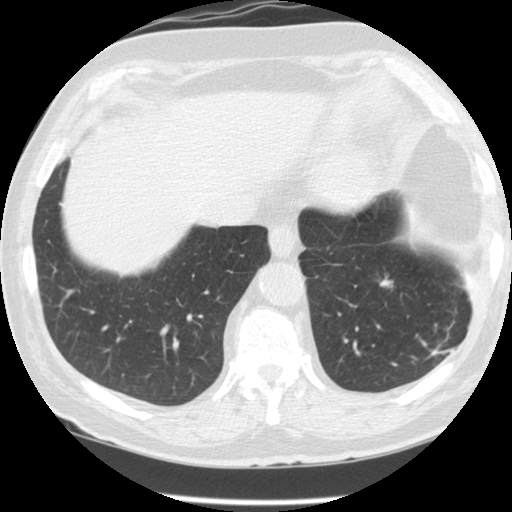
Low-dose screening chest CT, one axial slice; slice 34 of 127 in the series (ordered by position); reconstruction kernel STANDARD; lung window (W 1500 / L -600 HU); 2.5 mm slice thickness; 512 × 512 image matrix.
Annotated regions visible in this slice (outlined manually by an expert reader):
- lesion 1 (tumor, lower lobe of left lung): box from (x=380, y=280) to (x=392, y=286) px